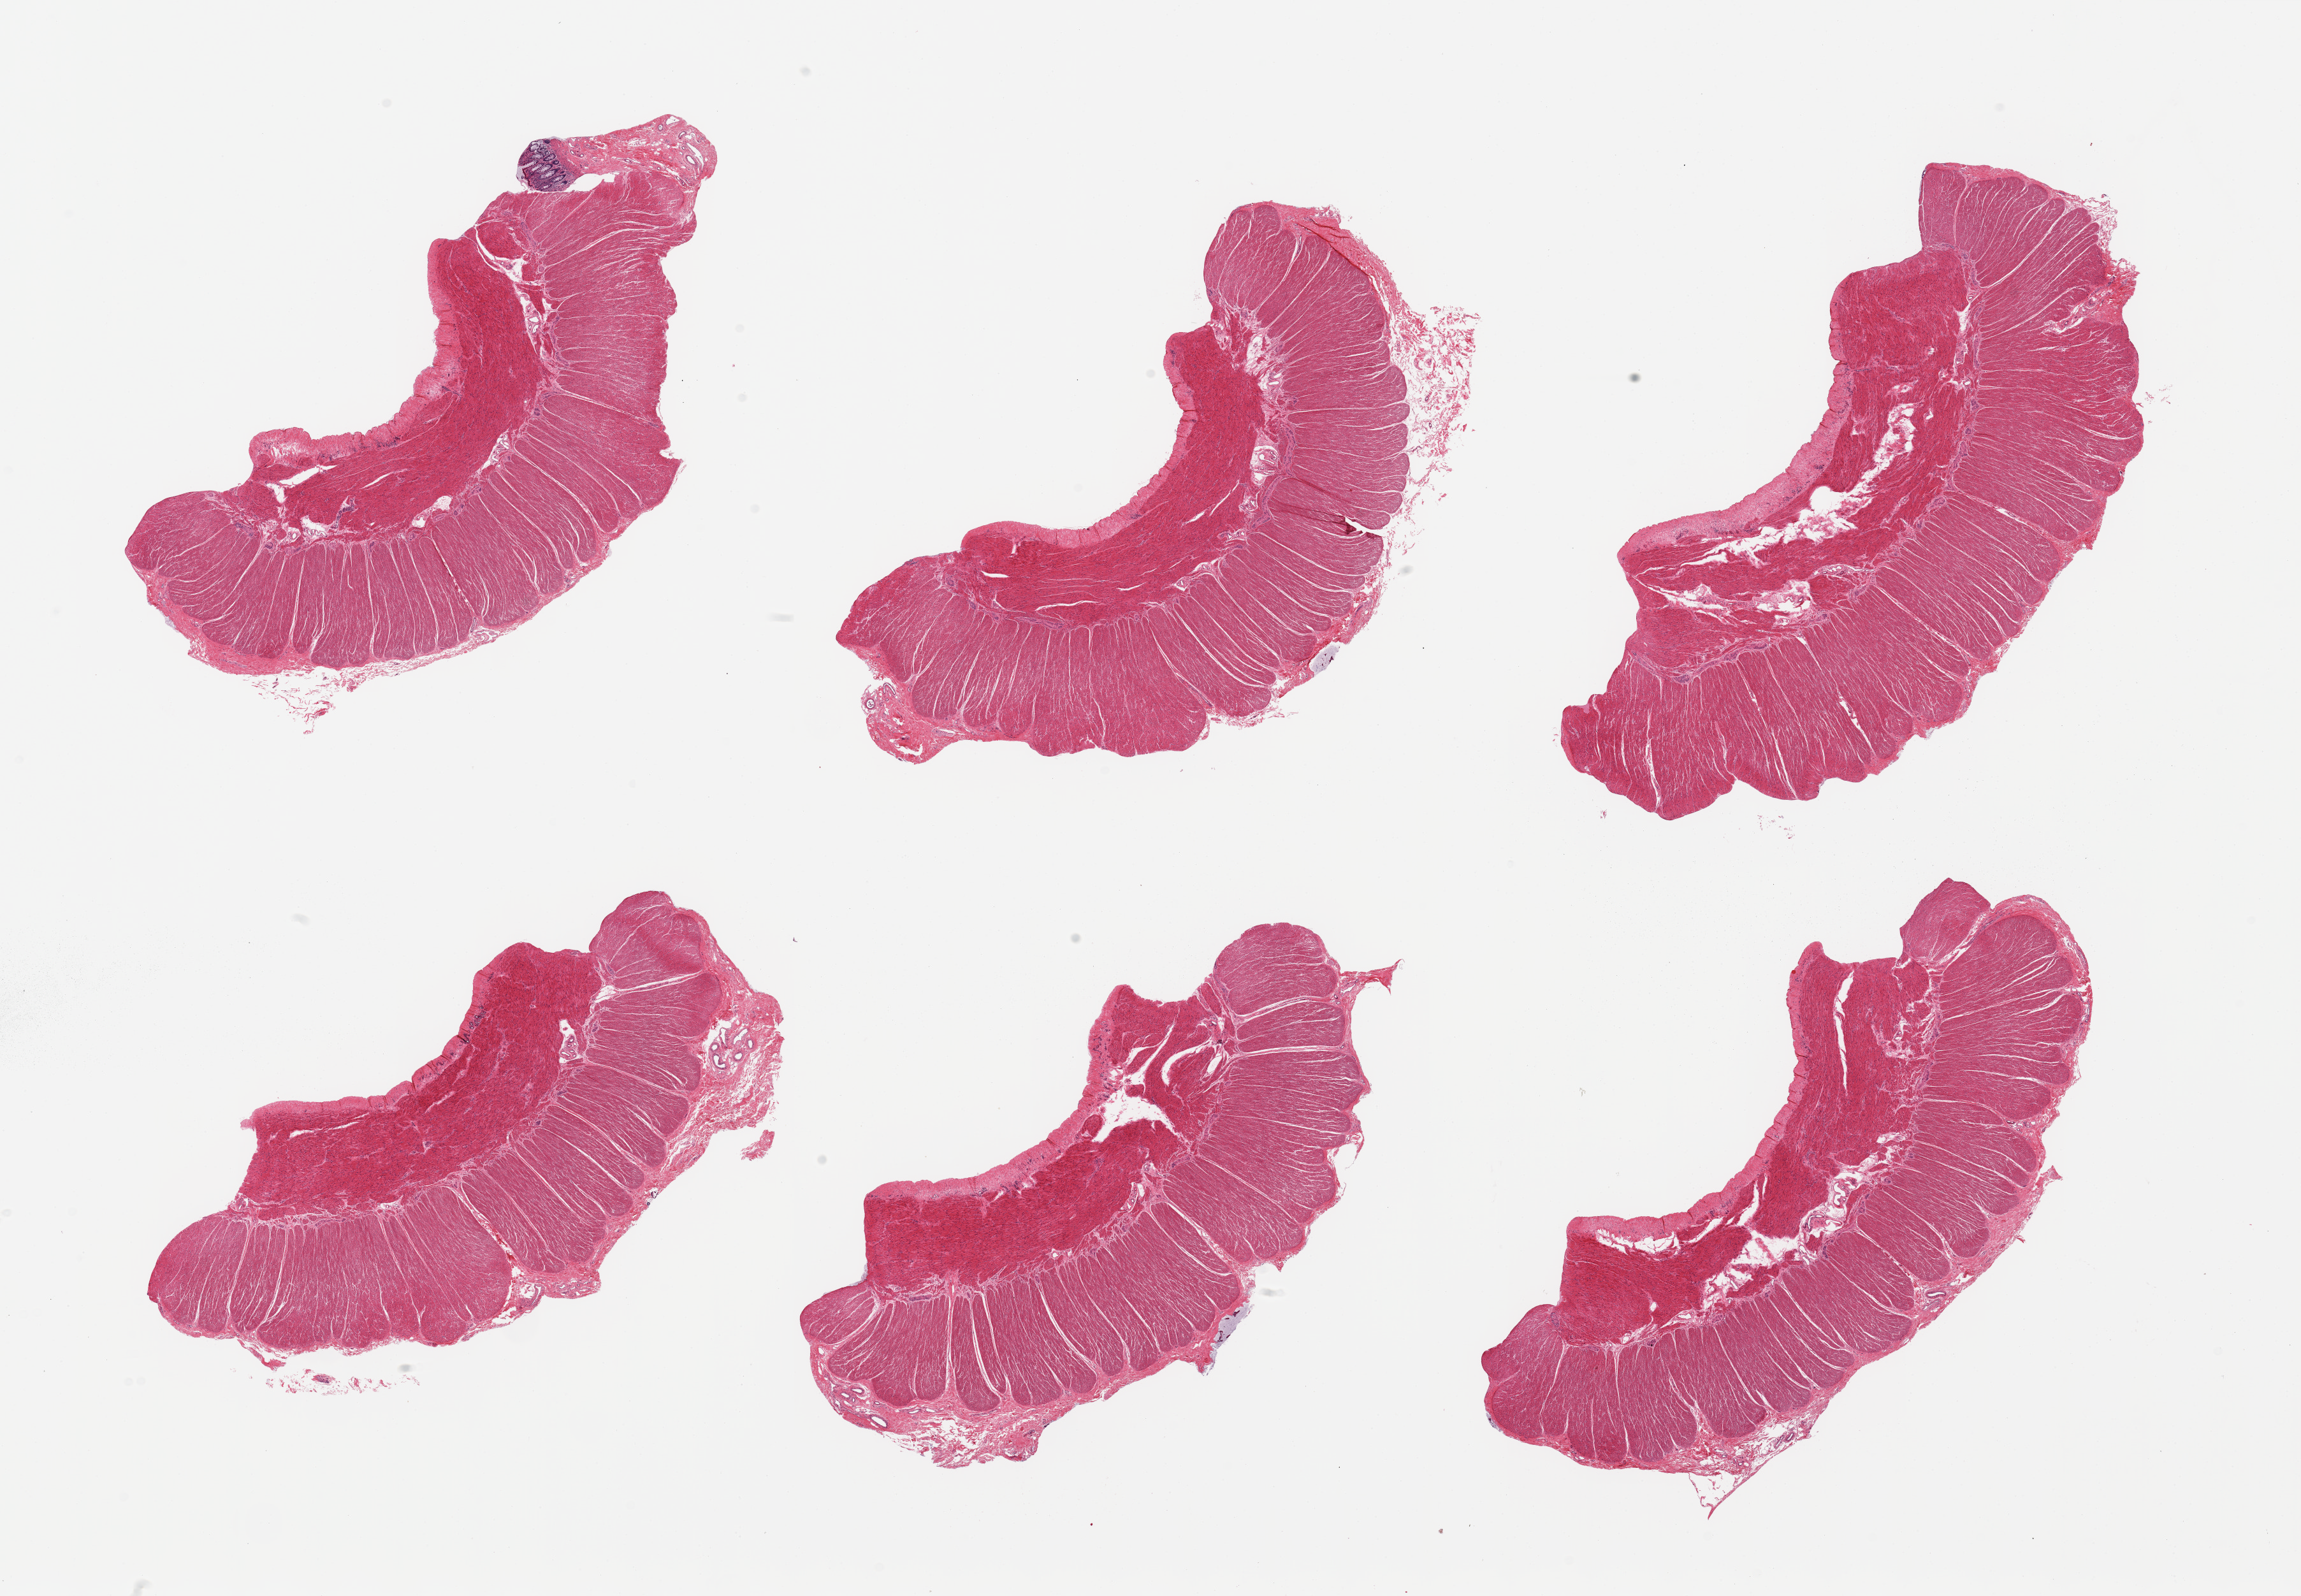
H&E whole-slide image, brightfield, a low-resolution overview of the entire scanned area, about 28.5 x 19.8 mm (slide scanned at 20x); PAXgene-fixed paraffin-embedded (PFPE) section; sampled site (target tissue): sigmoid colon; donor tissue sample. Female donor.
• review note (as recorded): 6 pieces, all muscularis, good specimens